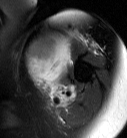
MRI of an extremity soft-tissue mass, one axial slice; position 56 of 87 along the scan axis; T2-weighted fat-saturated; MR volume resampled by the dataset authors to the PET/CT grid (not the native acquisition matrix); 127 × 138 image matrix. Female patient. From the clinical record (not read from this slice): histological type: pleiomorphic leiomyosarcoma; grade: high; site of the primary tumour: left biceps.
Structures marked on this image (expert contour drawn on MRI and transferred to this co-registered scan by the dataset authors):
- gross tumour volume including surrounding oedema: bounding box <27,32,73,102> (left, top, right, bottom; pixels)
- gross tumour volume (mass): <27,32,71,88>